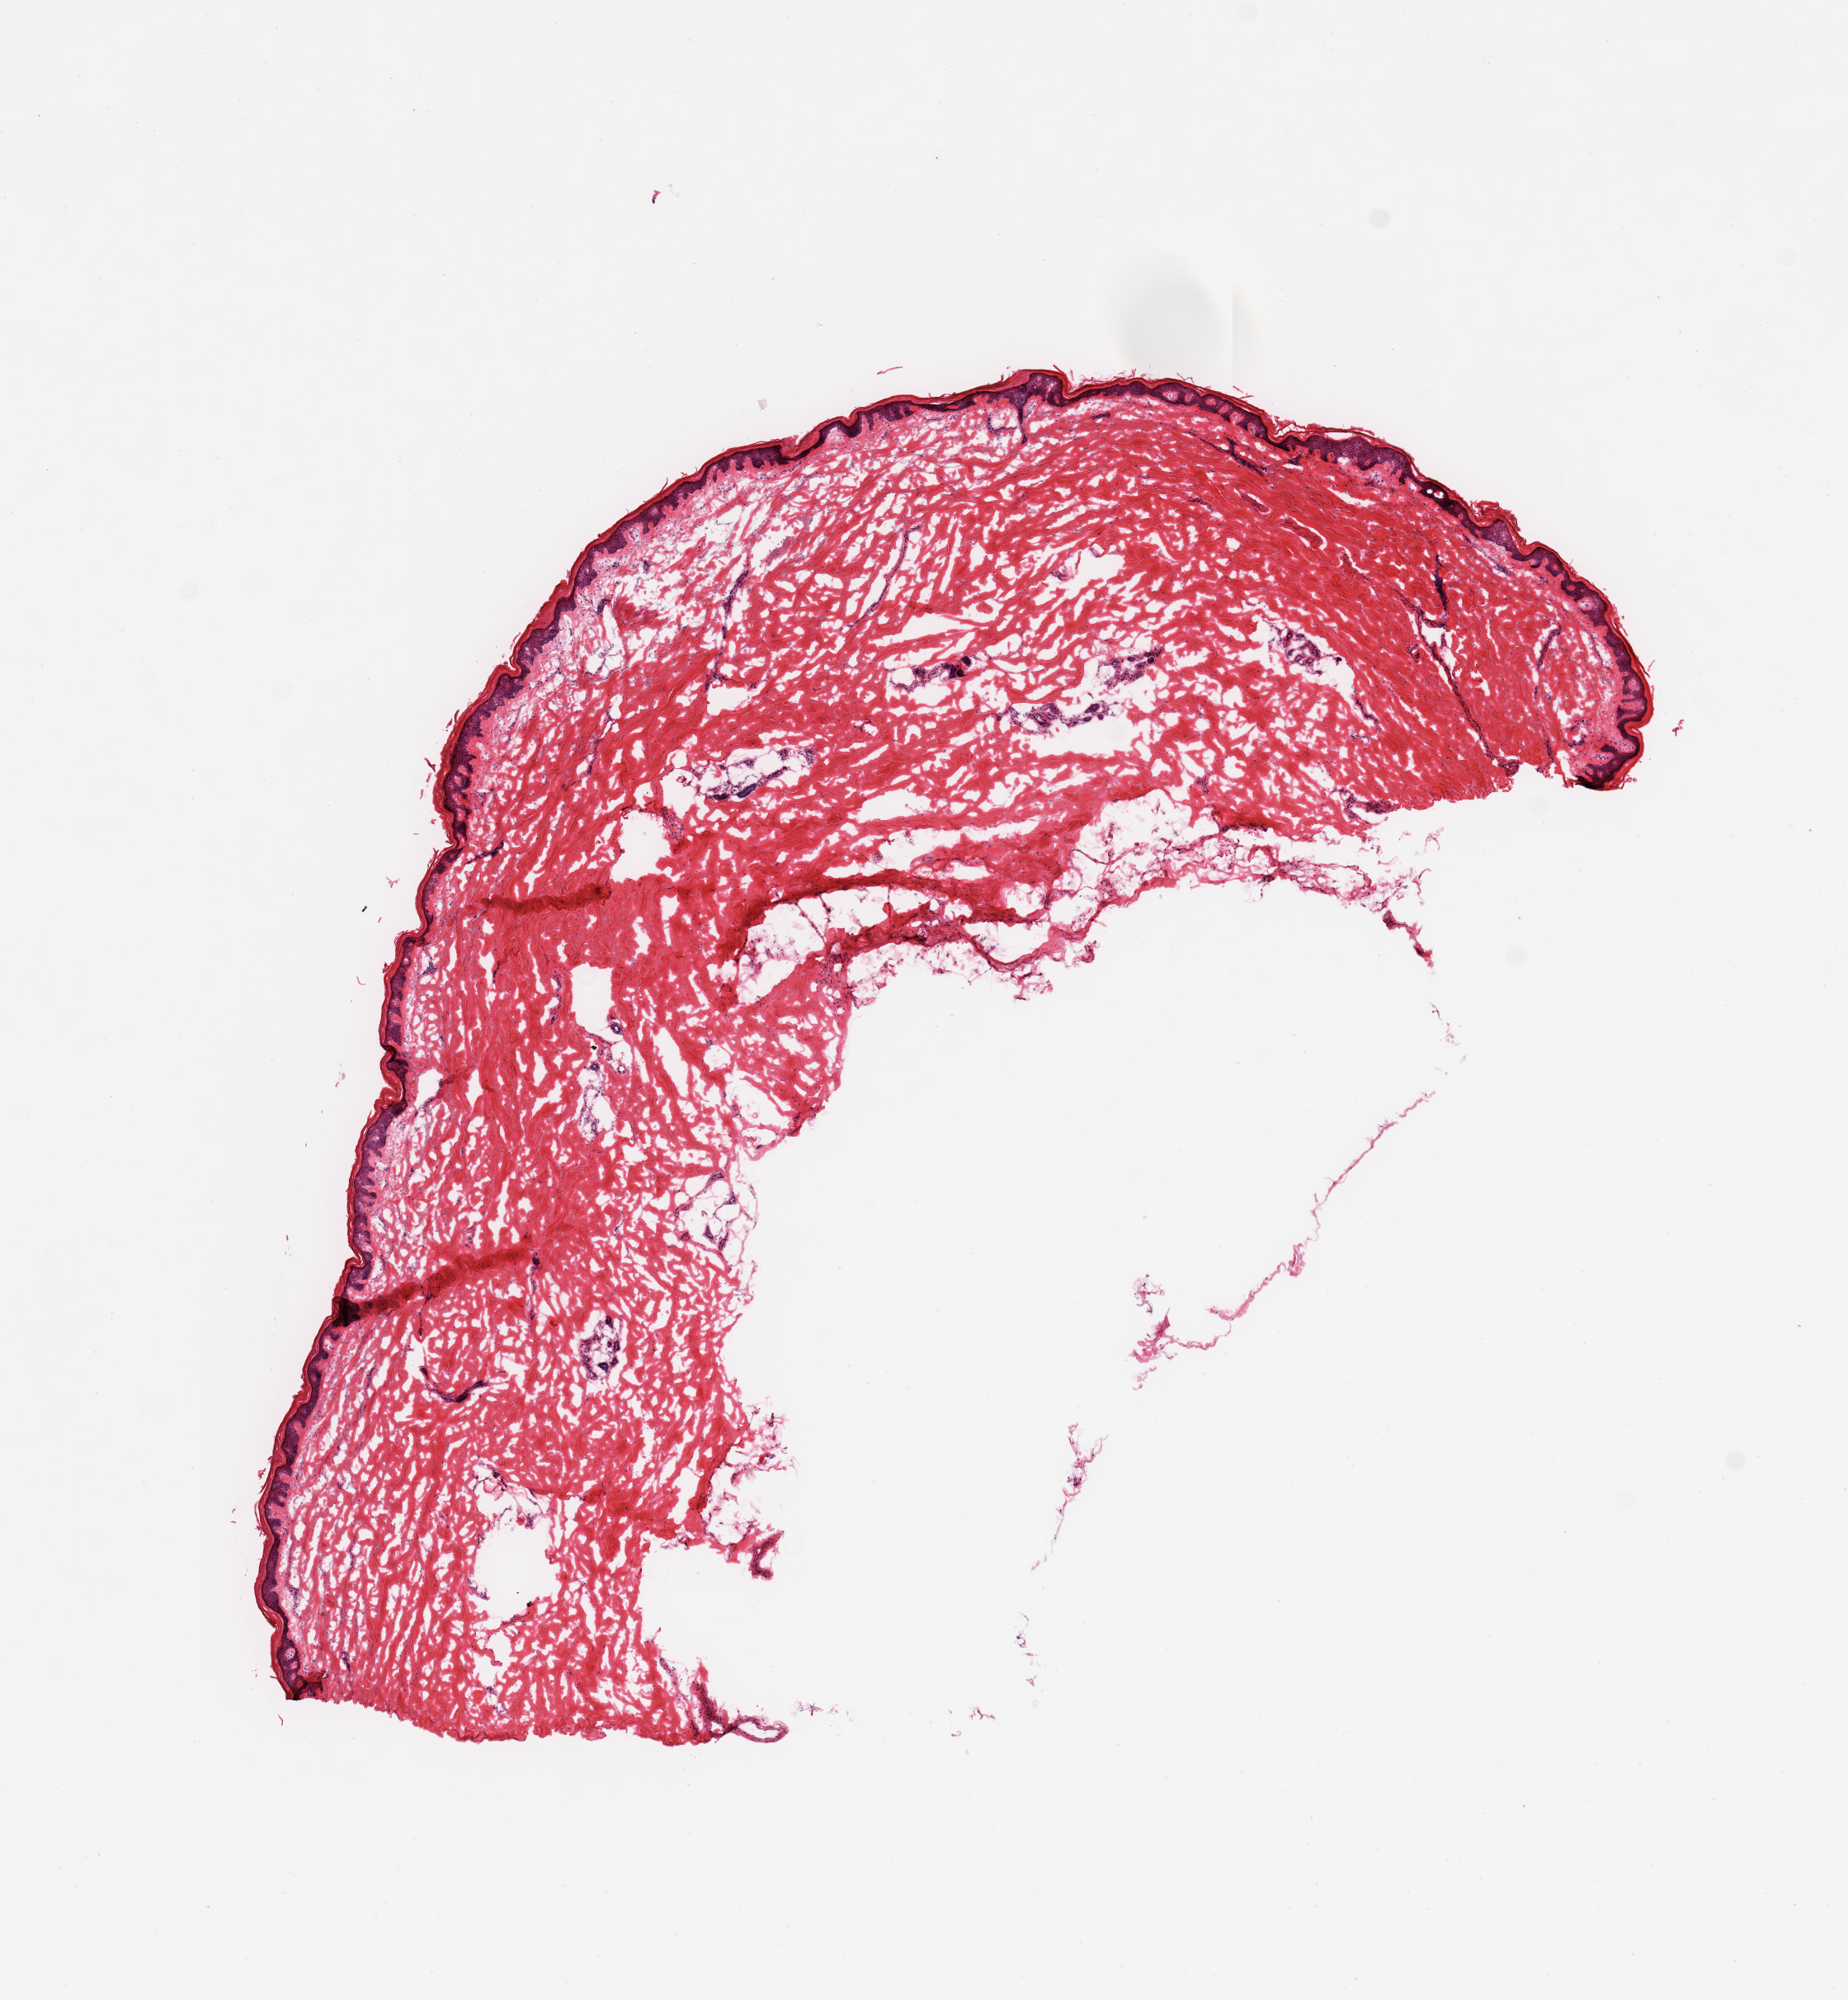
Whole-slide image, H&E stain, brightfield — a low-resolution overview of the entire scanned area, about 8.9 x 9.6 mm. Donor: male.
- specimen: frozen section (dry ice); target tissue: skin of lower leg; donor tissue sample